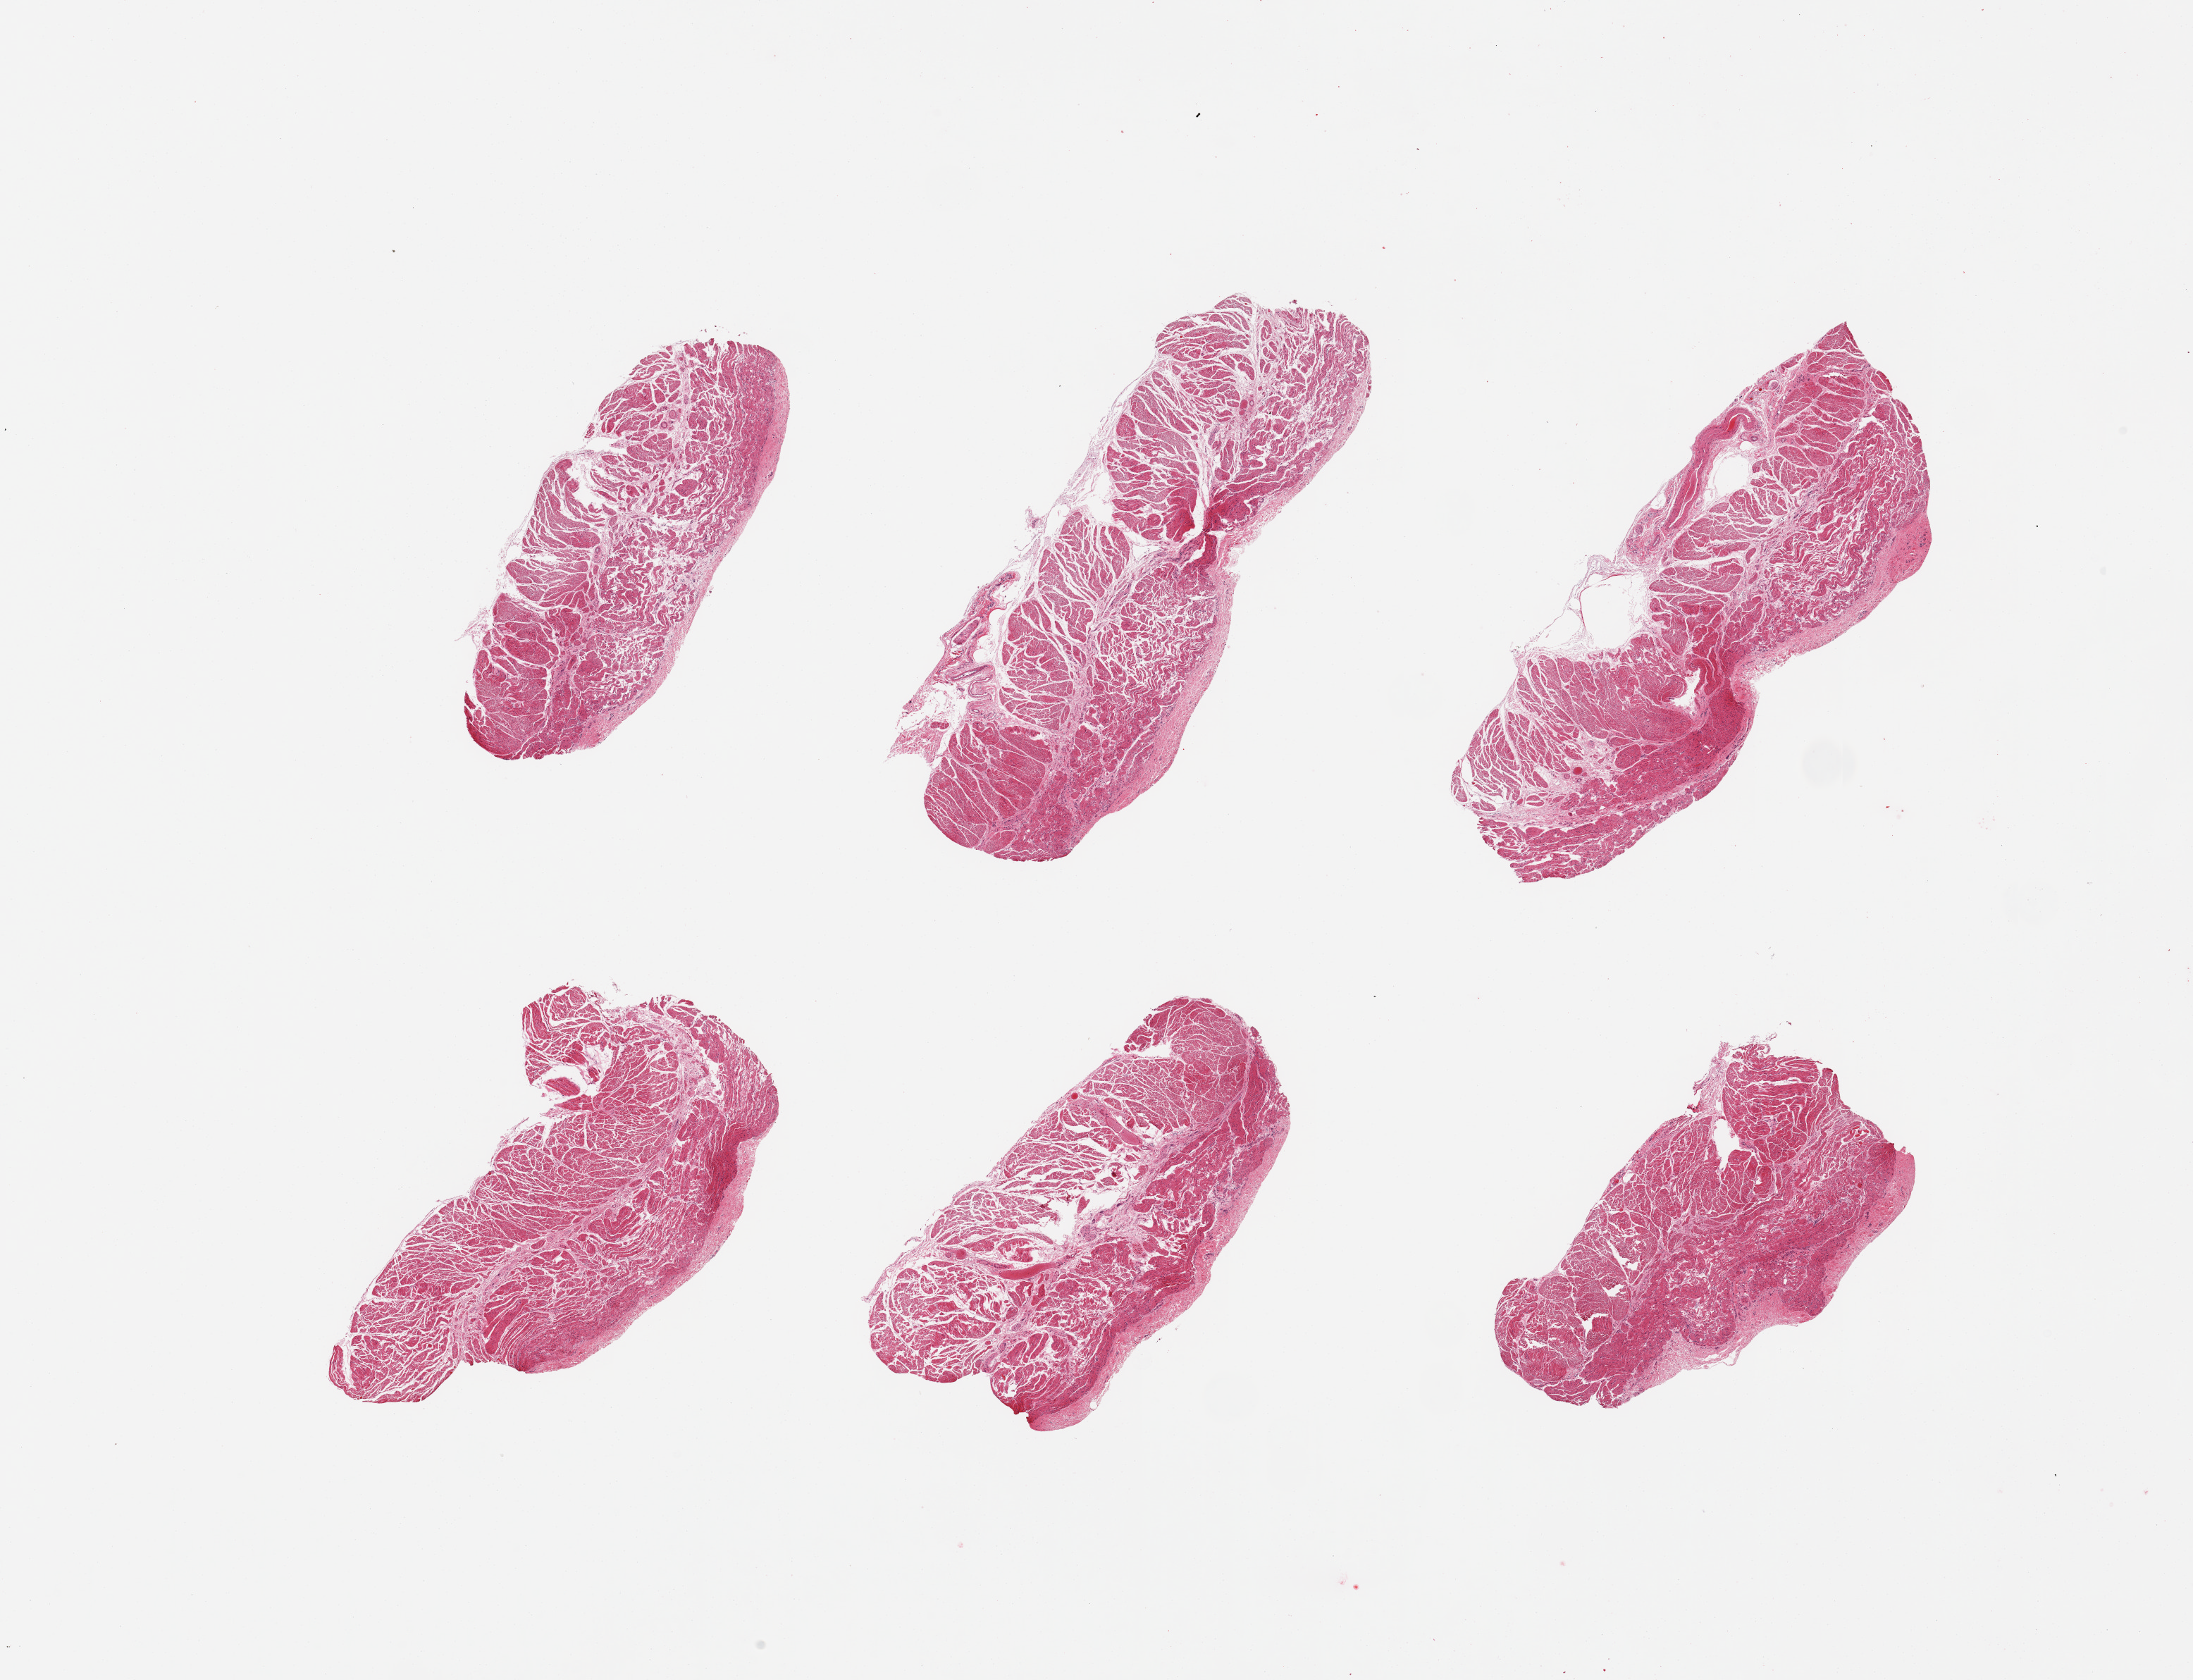
Whole-slide image, hematoxylin and eosin (H&E) stain, shown as a low-resolution overview of the whole scanned area (about 24.6 x 18.9 mm, slide scanned at 20x). PAXgene-fixed paraffin-embedded (PFPE) section. Target tissue: esophageal muscle. Tissue donor sample. Donor: male.
- pathologist's review note for this sample: 6 pieces; well dissected